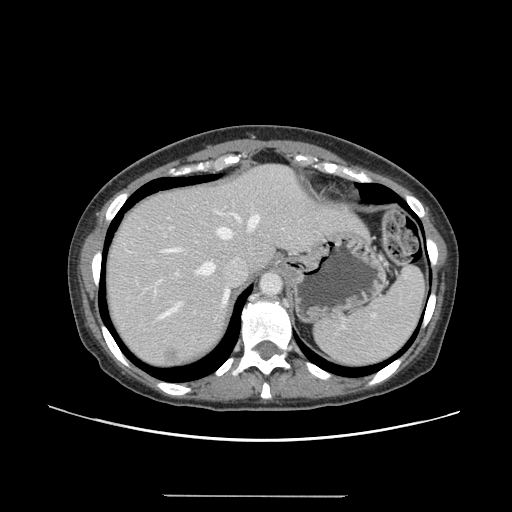
Contrast-enhanced abdominal CT, one axial slice. Position 116 of 144 along the scan axis. 120 kVp. Soft-tissue window (W 400 / L 40 HU). 2.5 mm slice thickness. 512 × 512 image matrix, field of view 380 × 380 mm. Female patient, age 53 years. From the clinical record (not read from this slice): diagnosis: colorectal cancer liver metastases, imaged before liver resection; multiple liver metastases: yes; largest metastasis: 1.1 cm; disease in both lobes: no.
Outlined on this slice (outlined manually by an expert reader):
- hepatic veins: bounding box <160,215,261,318> (left, top, right, bottom; pixels)
- liver: <106,165,364,367>
- planned liver remnant (the part of the liver to remain after resection): <105,165,289,299>
- portal vein (with intrahepatic branches): <156,227,178,284>
- liver metastasis: <164,349,179,363>